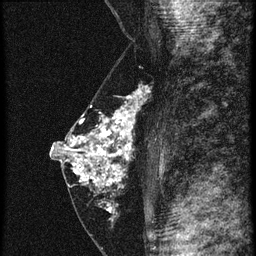
Breast MRI (dynamic contrast-enhanced), one sagittal slice. Slice 29 of 60 in the series (ordered by position). 4 images stored at this slice position (order not interpretable as contrast timing). 1.5 T. TE 4.2 ms, TR 20.4 ms. 256 × 256 image matrix, field of view 180 × 180 mm. Patient: female, 46 years. Case-level facts recorded for this patient, not image findings: setting: breast cancer imaged before/during neoadjuvant chemotherapy; receptor status: triple-negative.
Structures marked on this image (semi-automatically segmented with operator editing):
- analysis volume of interest (the breast-tissue region the enhancement analysis was run in; not a lesion): box from (x=67, y=88) to (x=150, y=201) px
- tumour enhancement mask (voxels above the 90 % enhancement threshold inside the analysis volume of interest): (x=67, y=94)–(x=141, y=187)